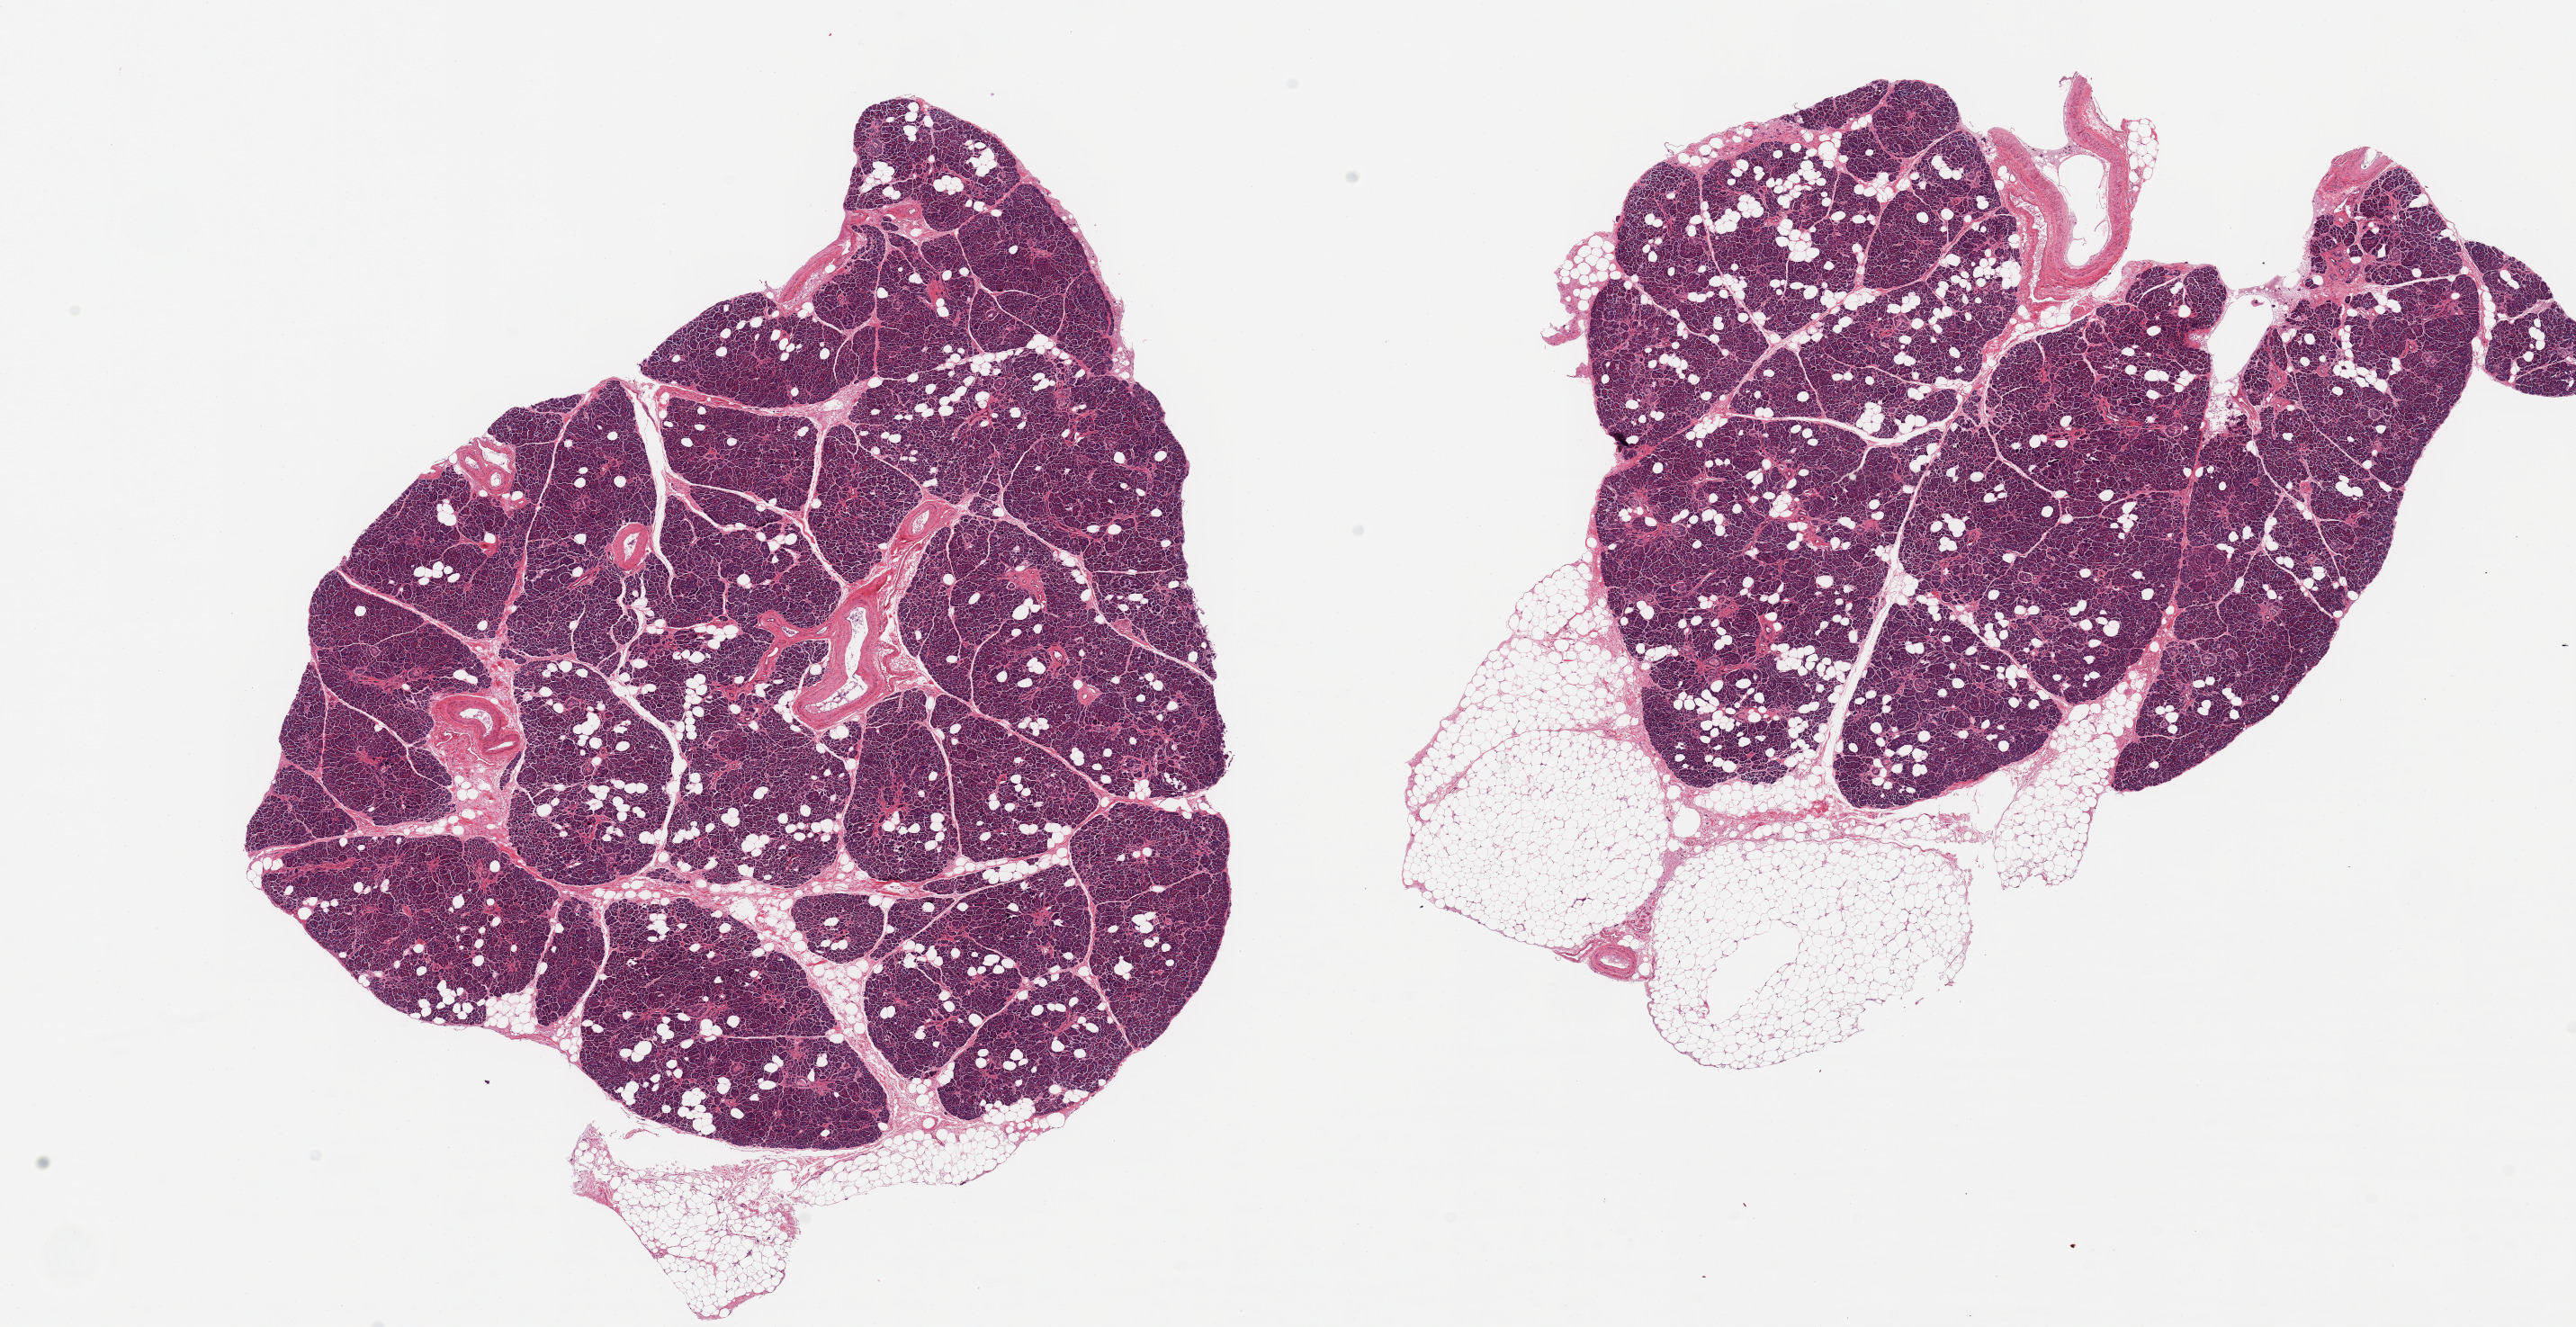
Digitized haematoxylin and eosin-stained section — a low-resolution overview of the entire scanned area, about 22.6 x 11.7 mm (from a 20x scan), PAXgene-fixed paraffin-embedded (PFPE) section, section of pancreas (target tissue), tissue donor sample. Donor: female.
* reviewer comment on this tissue sample: 2 pieces; 20% scattered internal fat on both; 30% external fat on 1